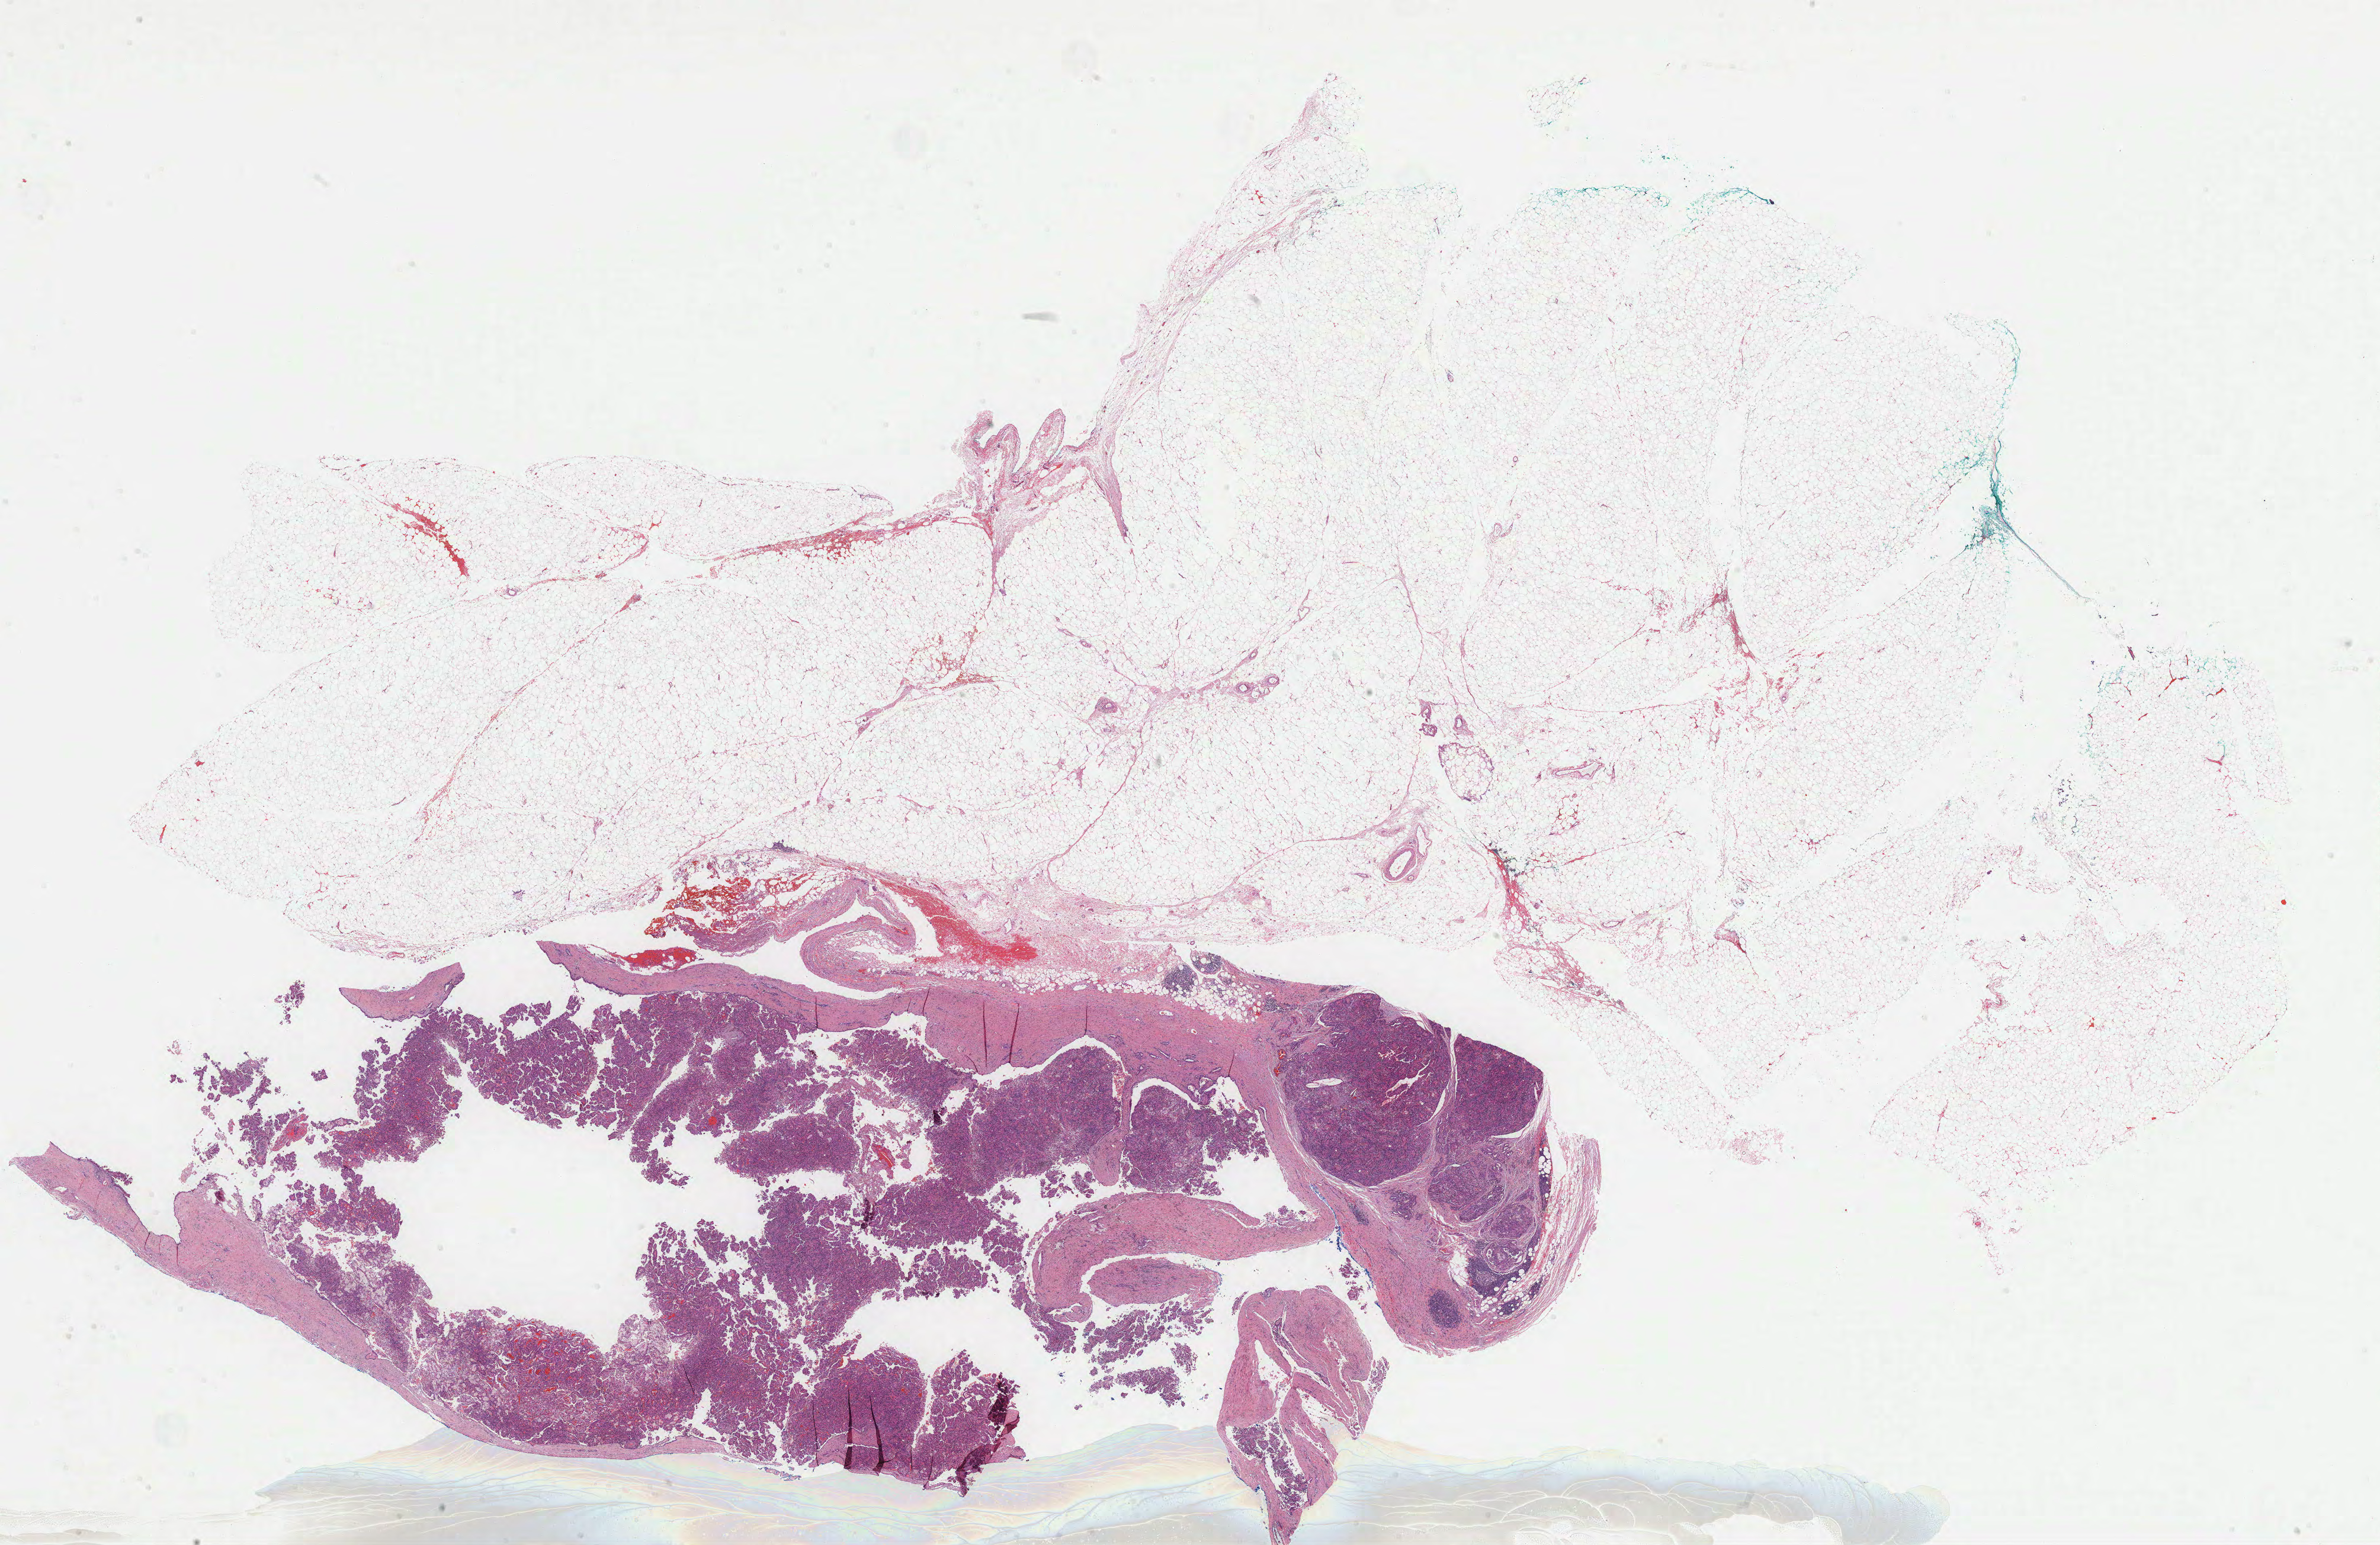
Digitized H&E-stained tissue section (whole slide) — low-resolution overview of the scanned area, about 32.5 x 21.1 mm; FFPE section; sample: primary tumour, kidney. Male patient; age at initial diagnosis 64 years.
- TNM: T1a NX MX
- pathologic diagnosis: Papillary adenocarcinoma, NOS
- AJCC pathologic stage: I